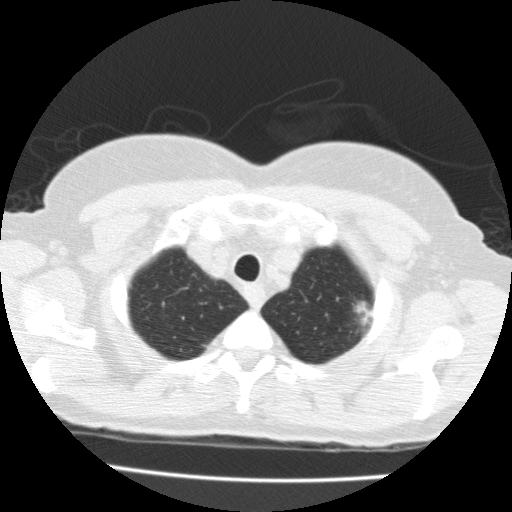
Low-dose screening chest CT, one axial slice. Slice 162 of 183 in the series (ordered by position). Reconstruction kernel FC10. 120 kVp. Lung window (W 1500 / L -600 HU). 2 mm slice thickness. 512 × 512 image matrix.
Structures marked on this image (manually delineated by an expert):
- lesion 1 (tumor, upper lobe of left lung): bounding box [x1, y1, x2, y2] px = [355, 301, 374, 326]